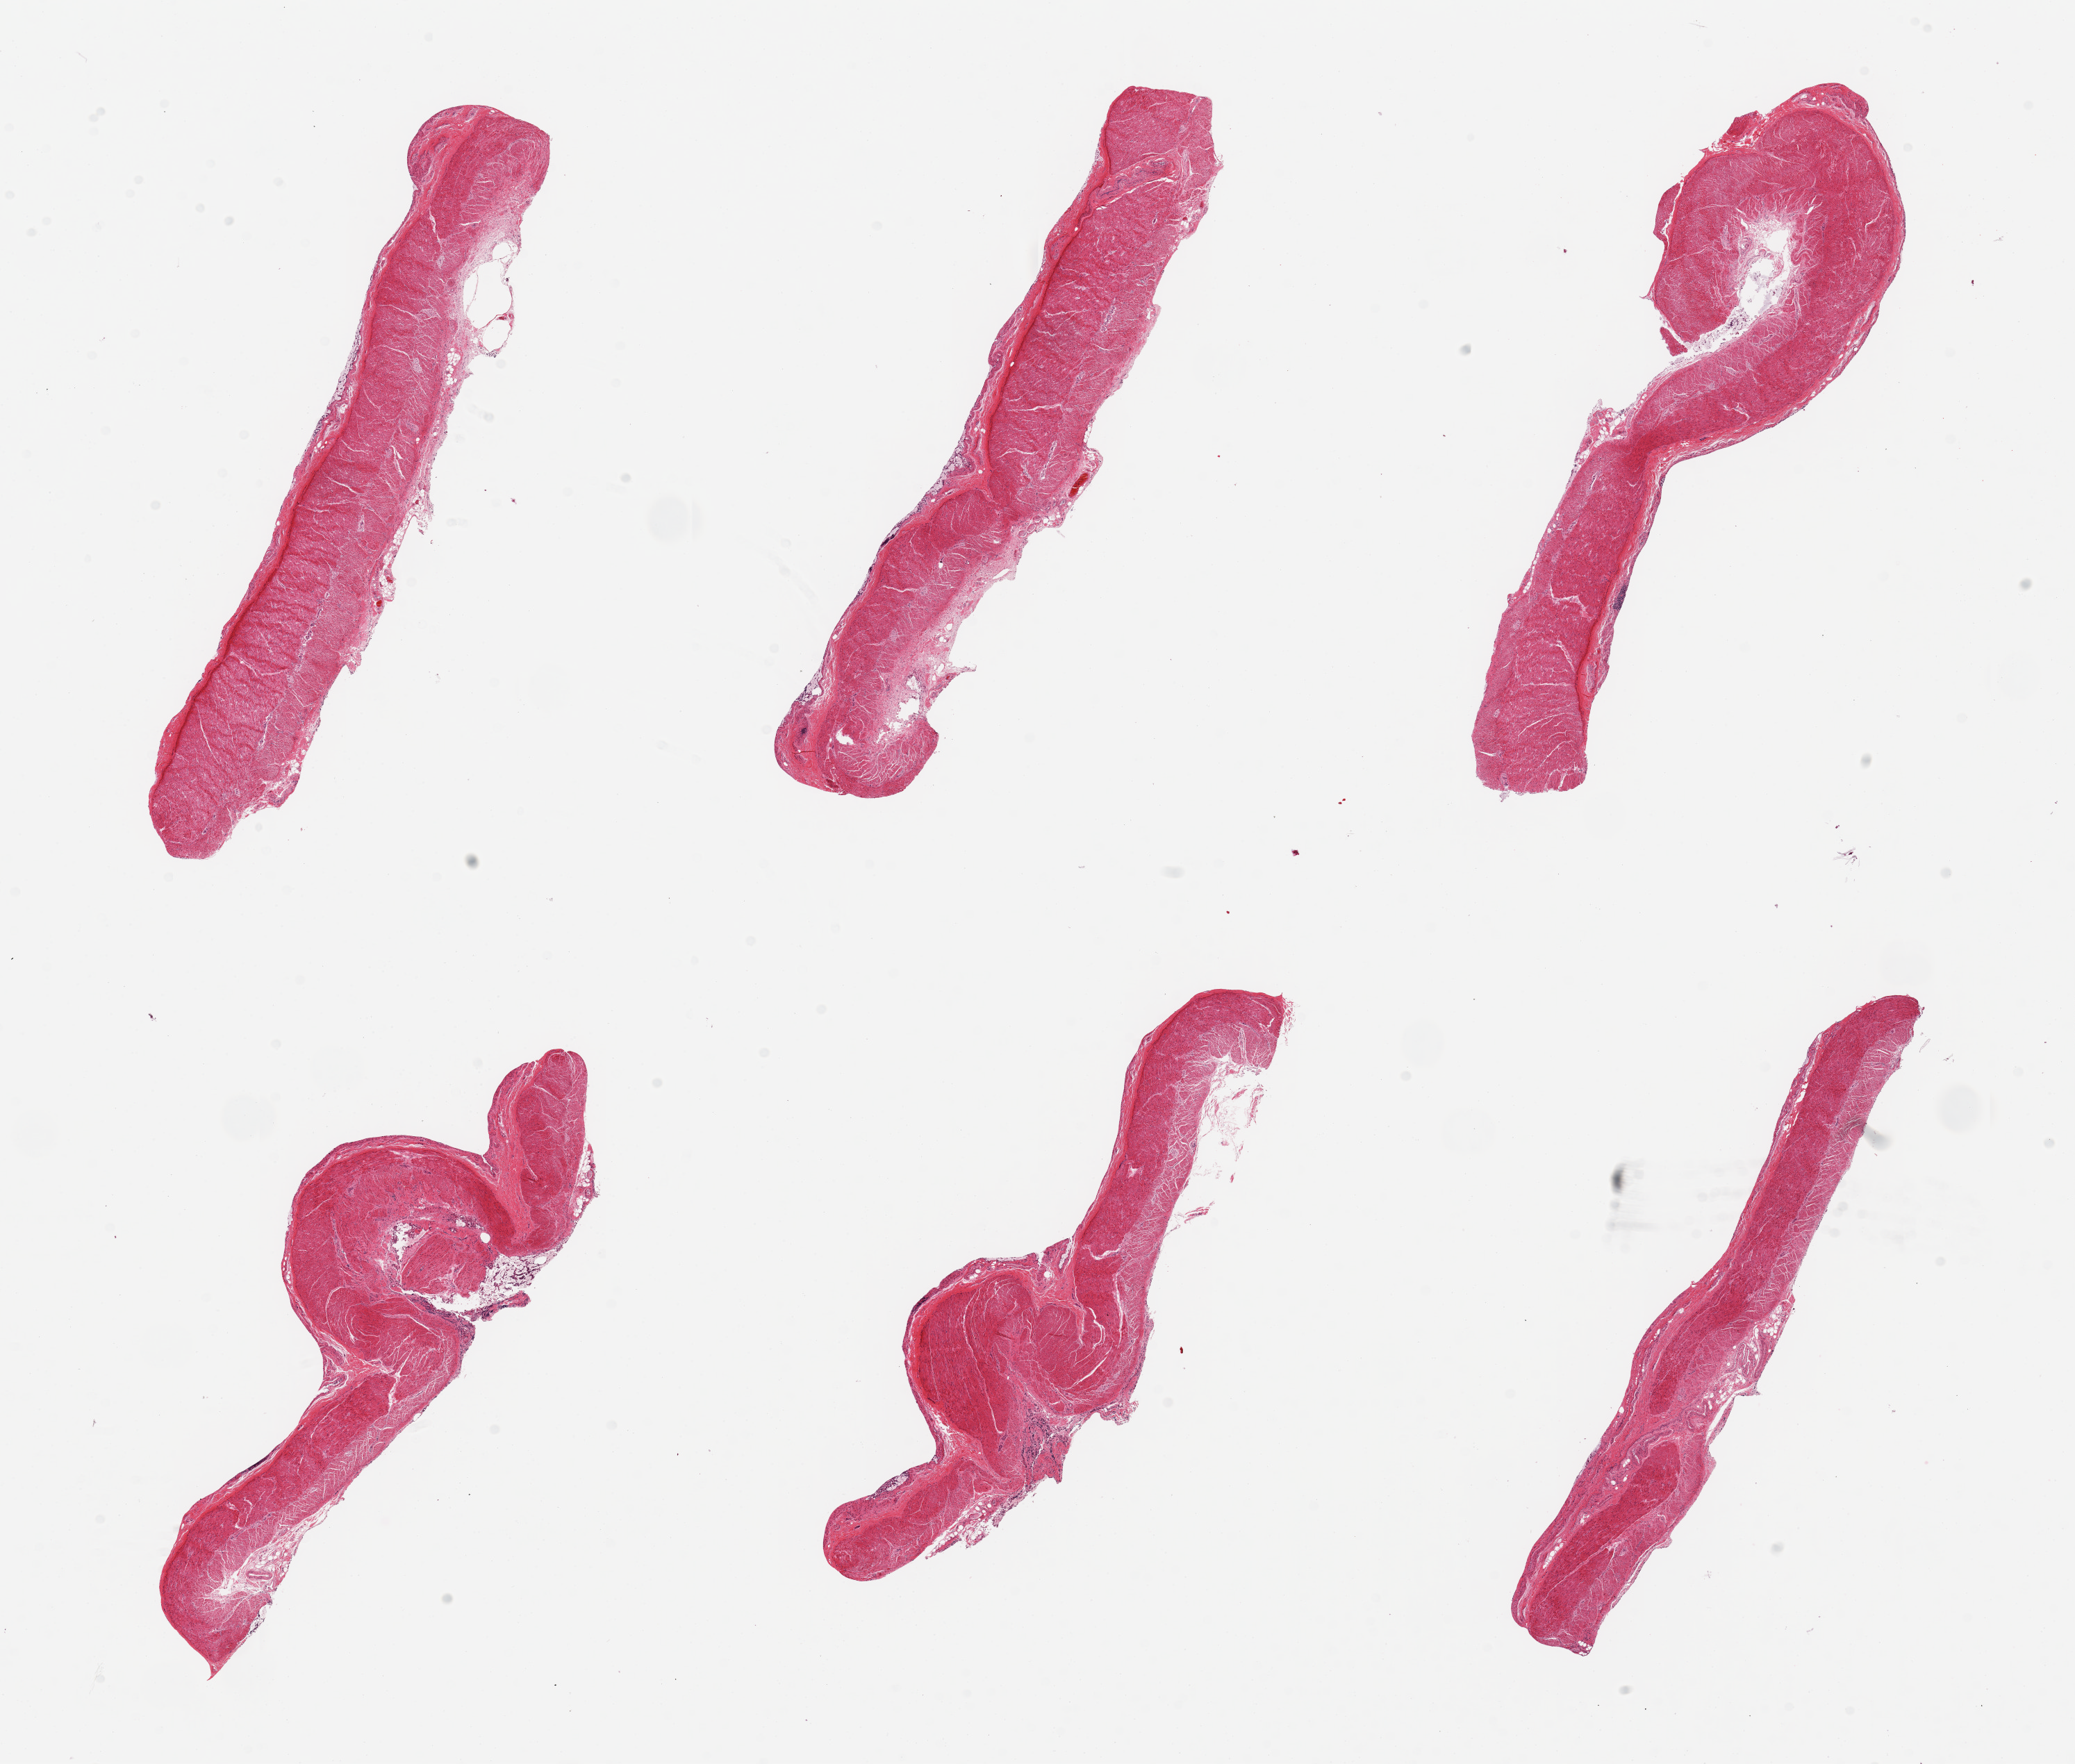
Hematoxylin and eosin (H&E) whole-slide image — whole scanned area (about 23.6 x 20.1 mm) shown as a low-resolution overview, PAXgene-fixed paraffin-embedded (PFPE) section, section of sigmoid colon (target tissue), donor tissue sample. Donor: male.
• pathologist's review note for this sample: 6 pieces; well dissected muscularis